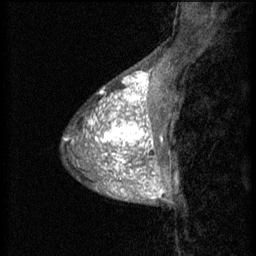
Breast MRI (dynamic contrast-enhanced), one sagittal slice; slice 16 of 60 in the series (ordered by position); 3 images stored at this slice position (order not interpretable as contrast timing); 1.5 T; TE 4.2 ms, TR 8.2 ms; 2 mm slice thickness; 256 × 256 image matrix, field of view 180 × 180 mm. Patient: female, 38 years.
Outlined on this slice (semi-automatic segmentation, software-assisted and operator-edited):
- analysis volume of interest (the breast-tissue region the enhancement analysis was run in; not a lesion): bounding box <95,106,157,171> (left, top, right, bottom; pixels)
- tumour enhancement mask (voxels above the 70 % enhancement threshold inside the analysis volume of interest): <95,106,157,171>